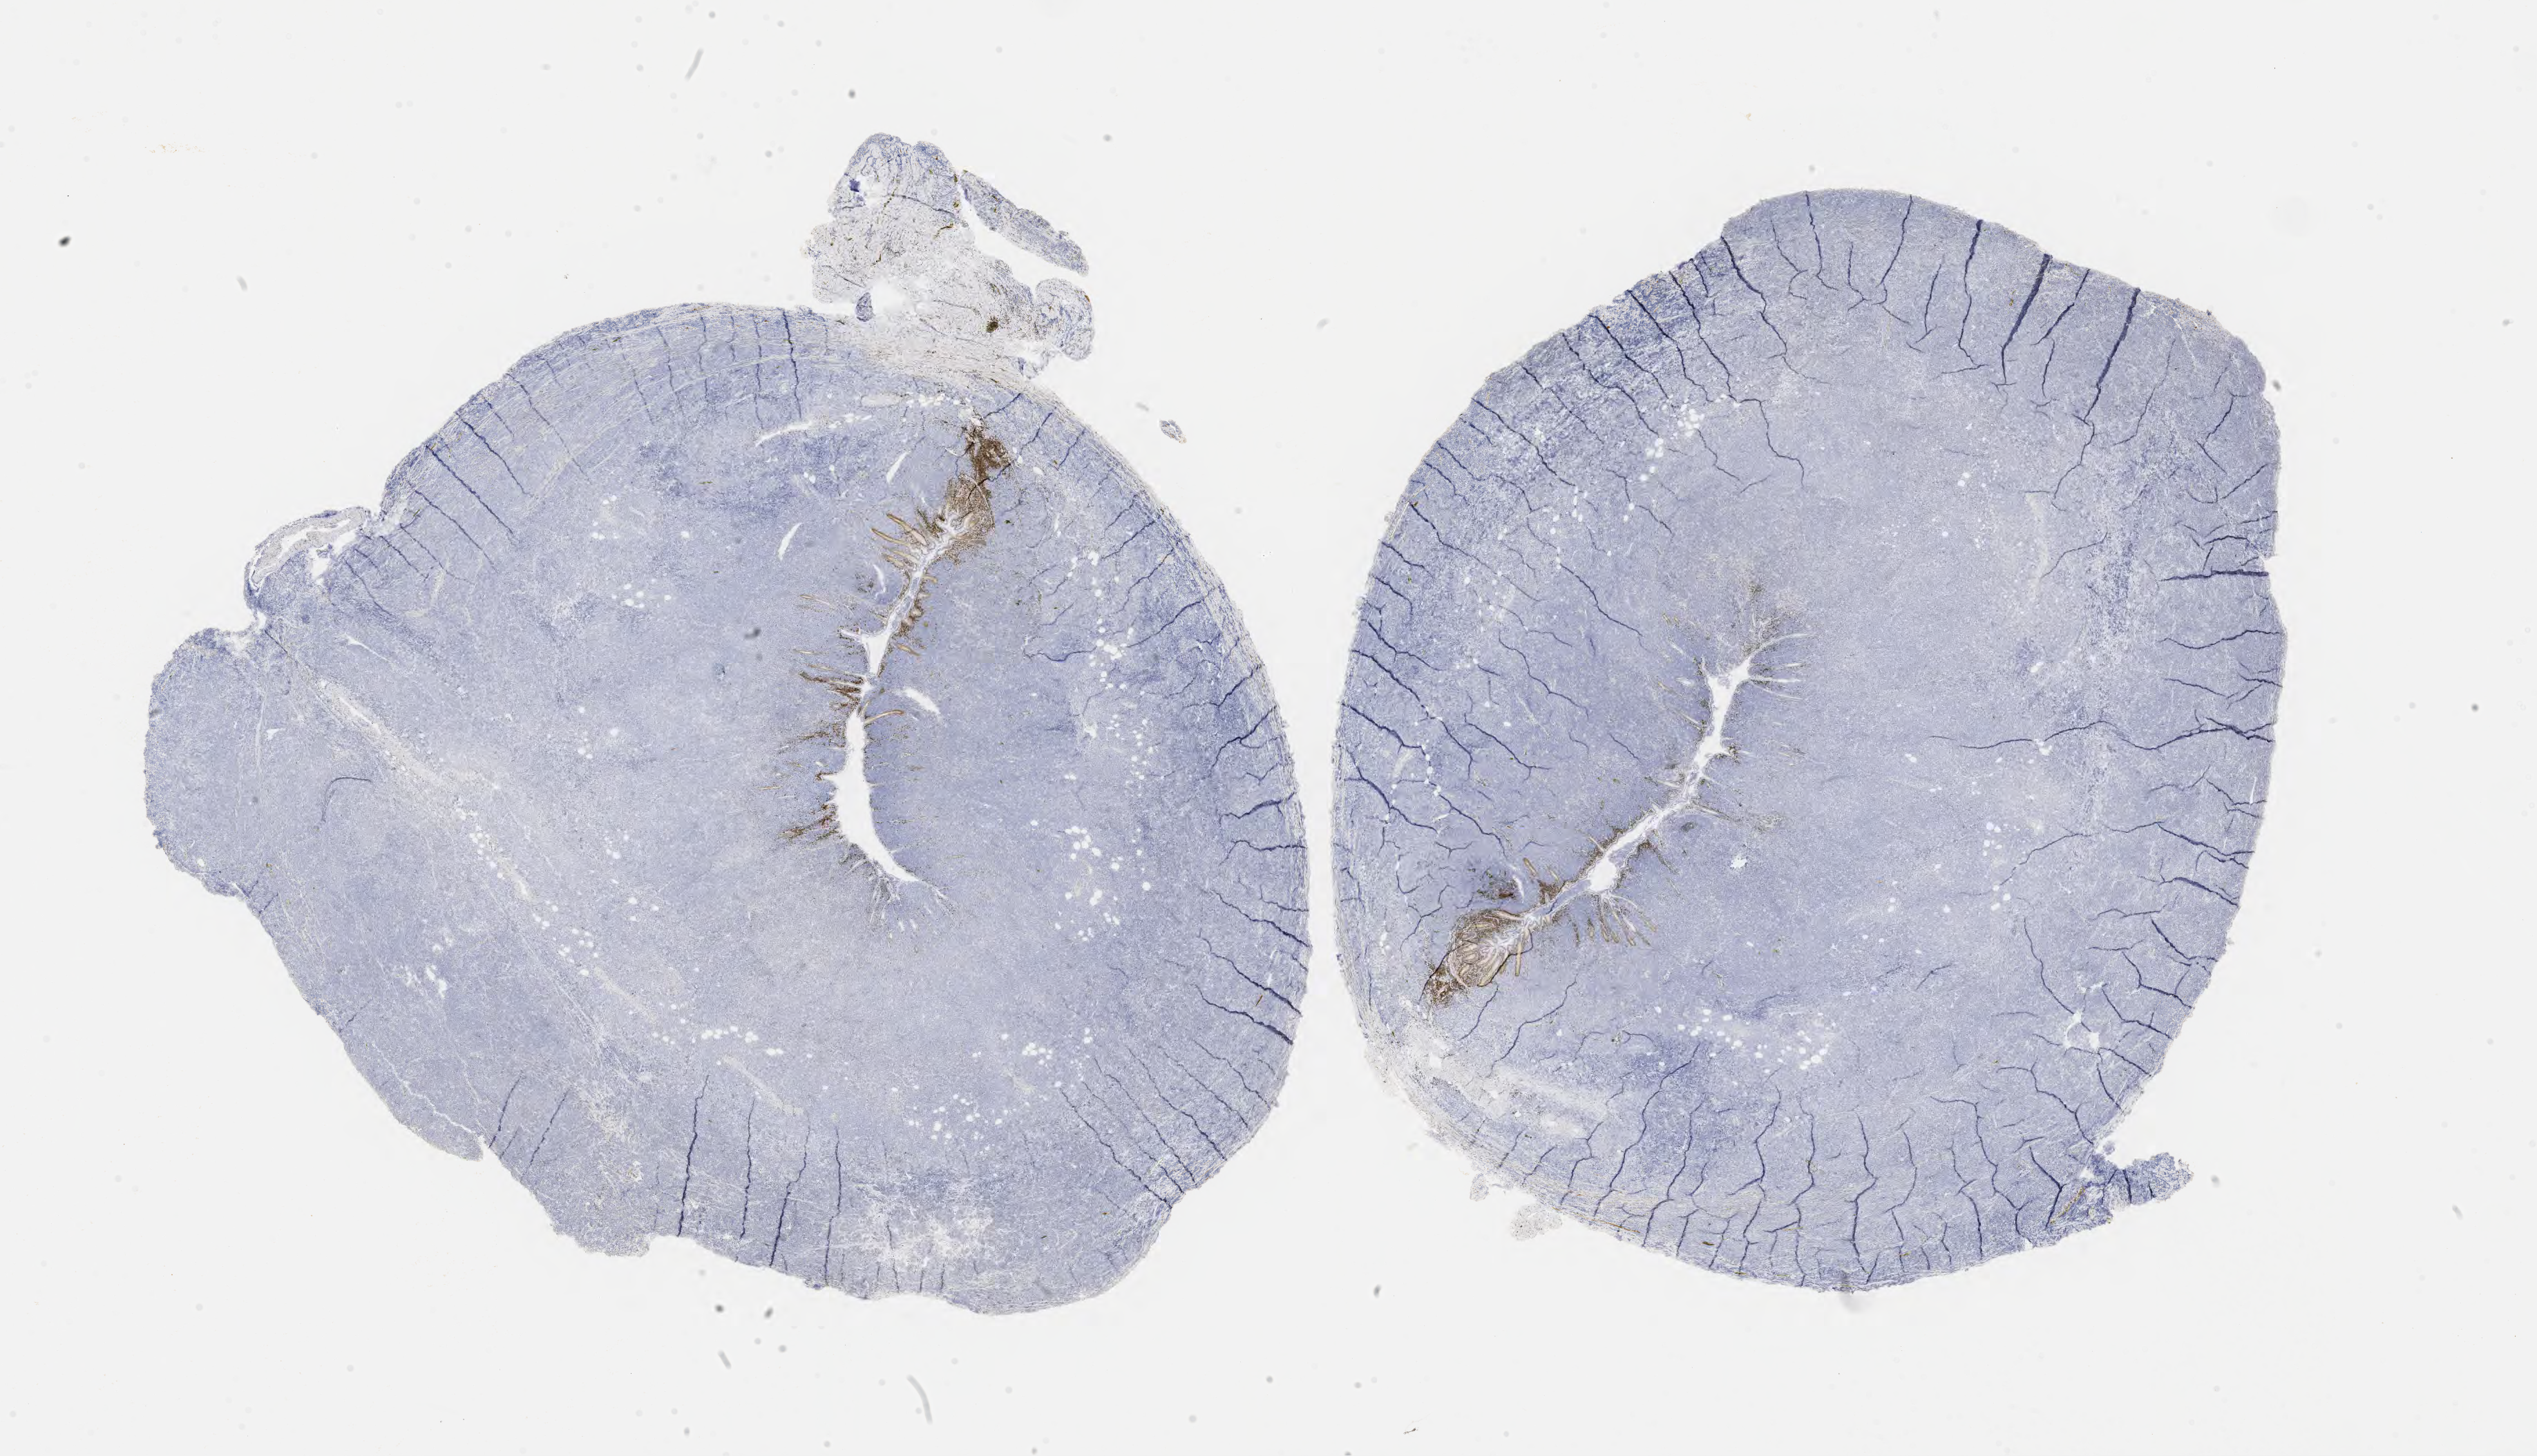
Whole-slide image, immunohistochemical stain for BCL2, low-resolution overview of the scanned area, about 29.7 x 17.0 mm; tumor tissue. Male patient, aged 63.
• histologic diagnosis: Diffuse large B-cell lymphoma, NOS